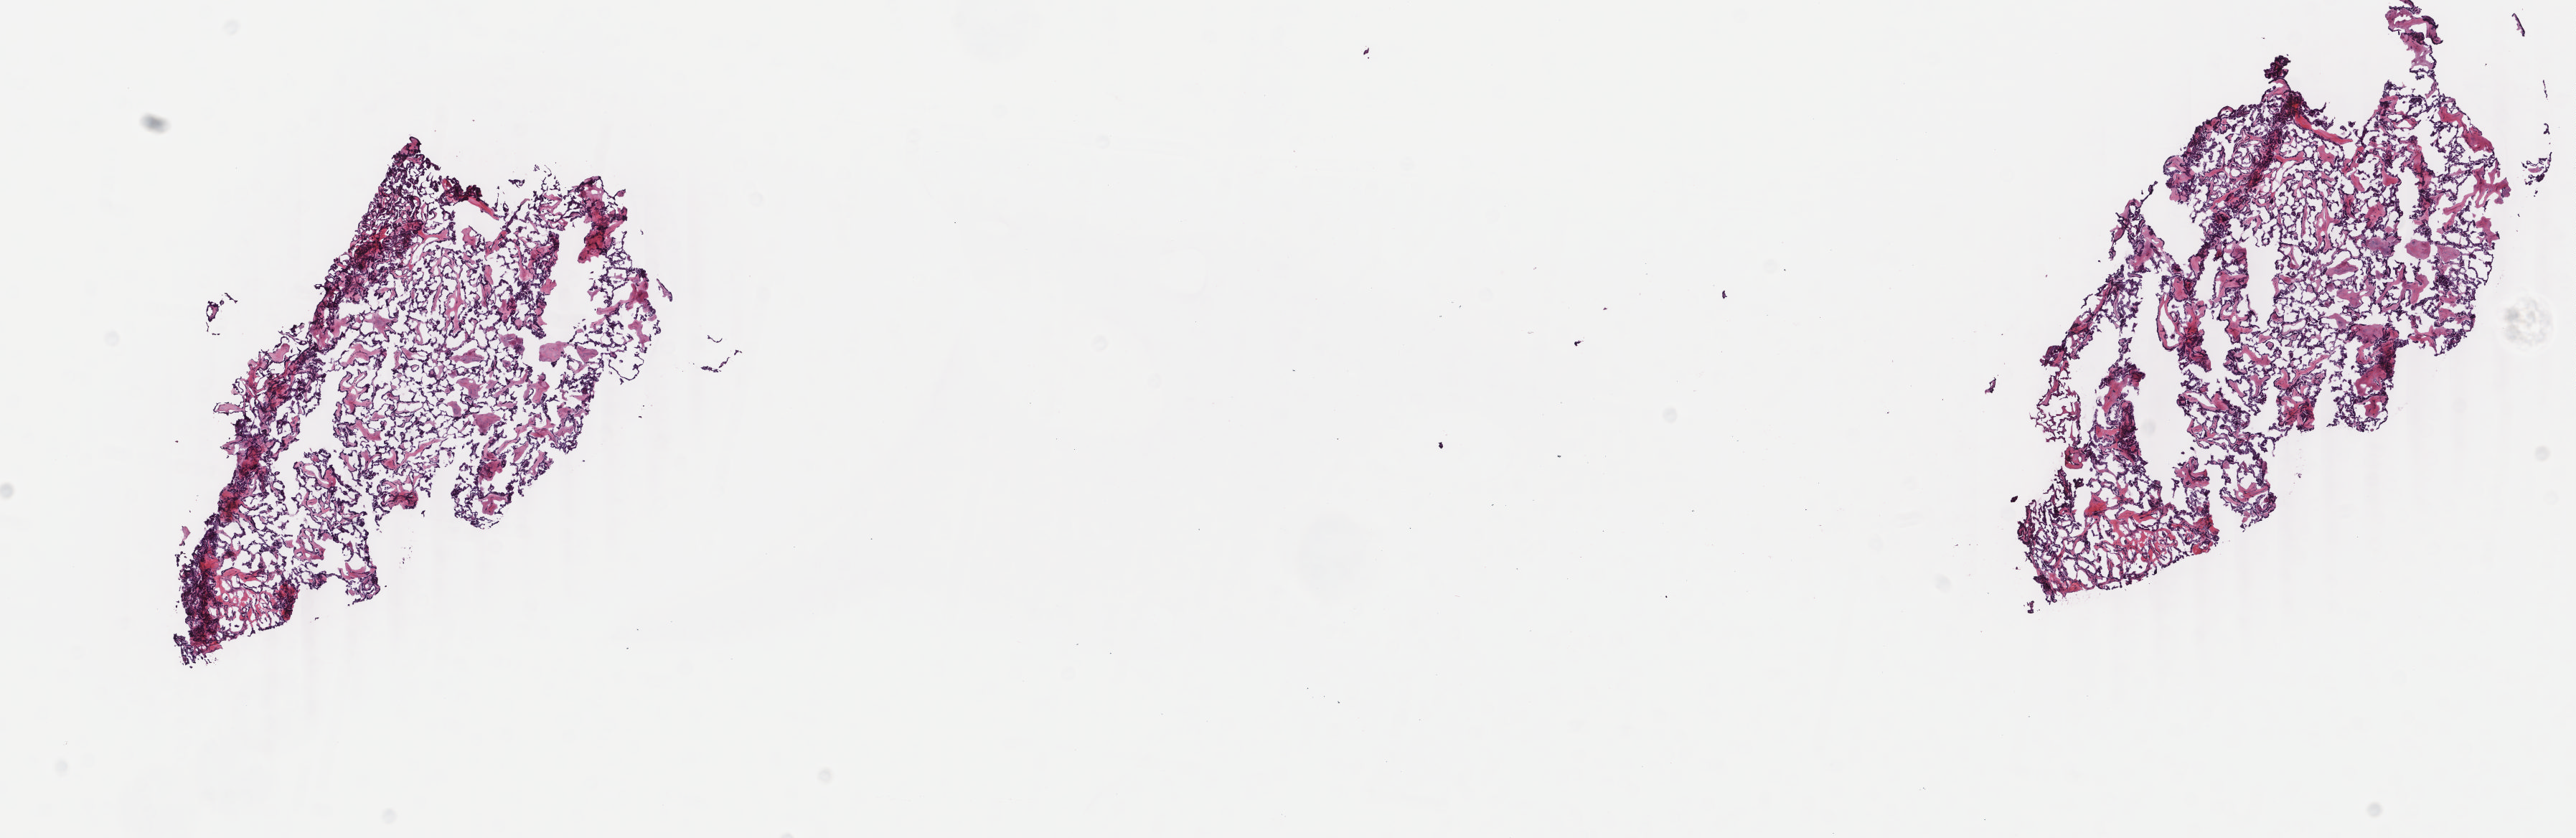
H&E whole-slide image, whole scanned area (about 14.3 x 4.6 mm) shown as a low-resolution overview; frozen section from the top of the tissue portion; thyroid, primary tumour sample. Female, age 60 years at initial diagnosis. Composition of this section per pathologist review: tumour cells 95%, tumour nuclei 99%, normal cells 0%, stromal cells 5%, necrosis 0%. Inflammatory infiltration, as recorded: lymphocyte infiltration 0%, monocyte infiltration 0%, neutrophil infiltration 0%.
AJCC pathologic stage: IVC (6th edition). Histologic diagnosis: Papillary adenocarcinoma, NOS. TNM: T4a N1b M1.